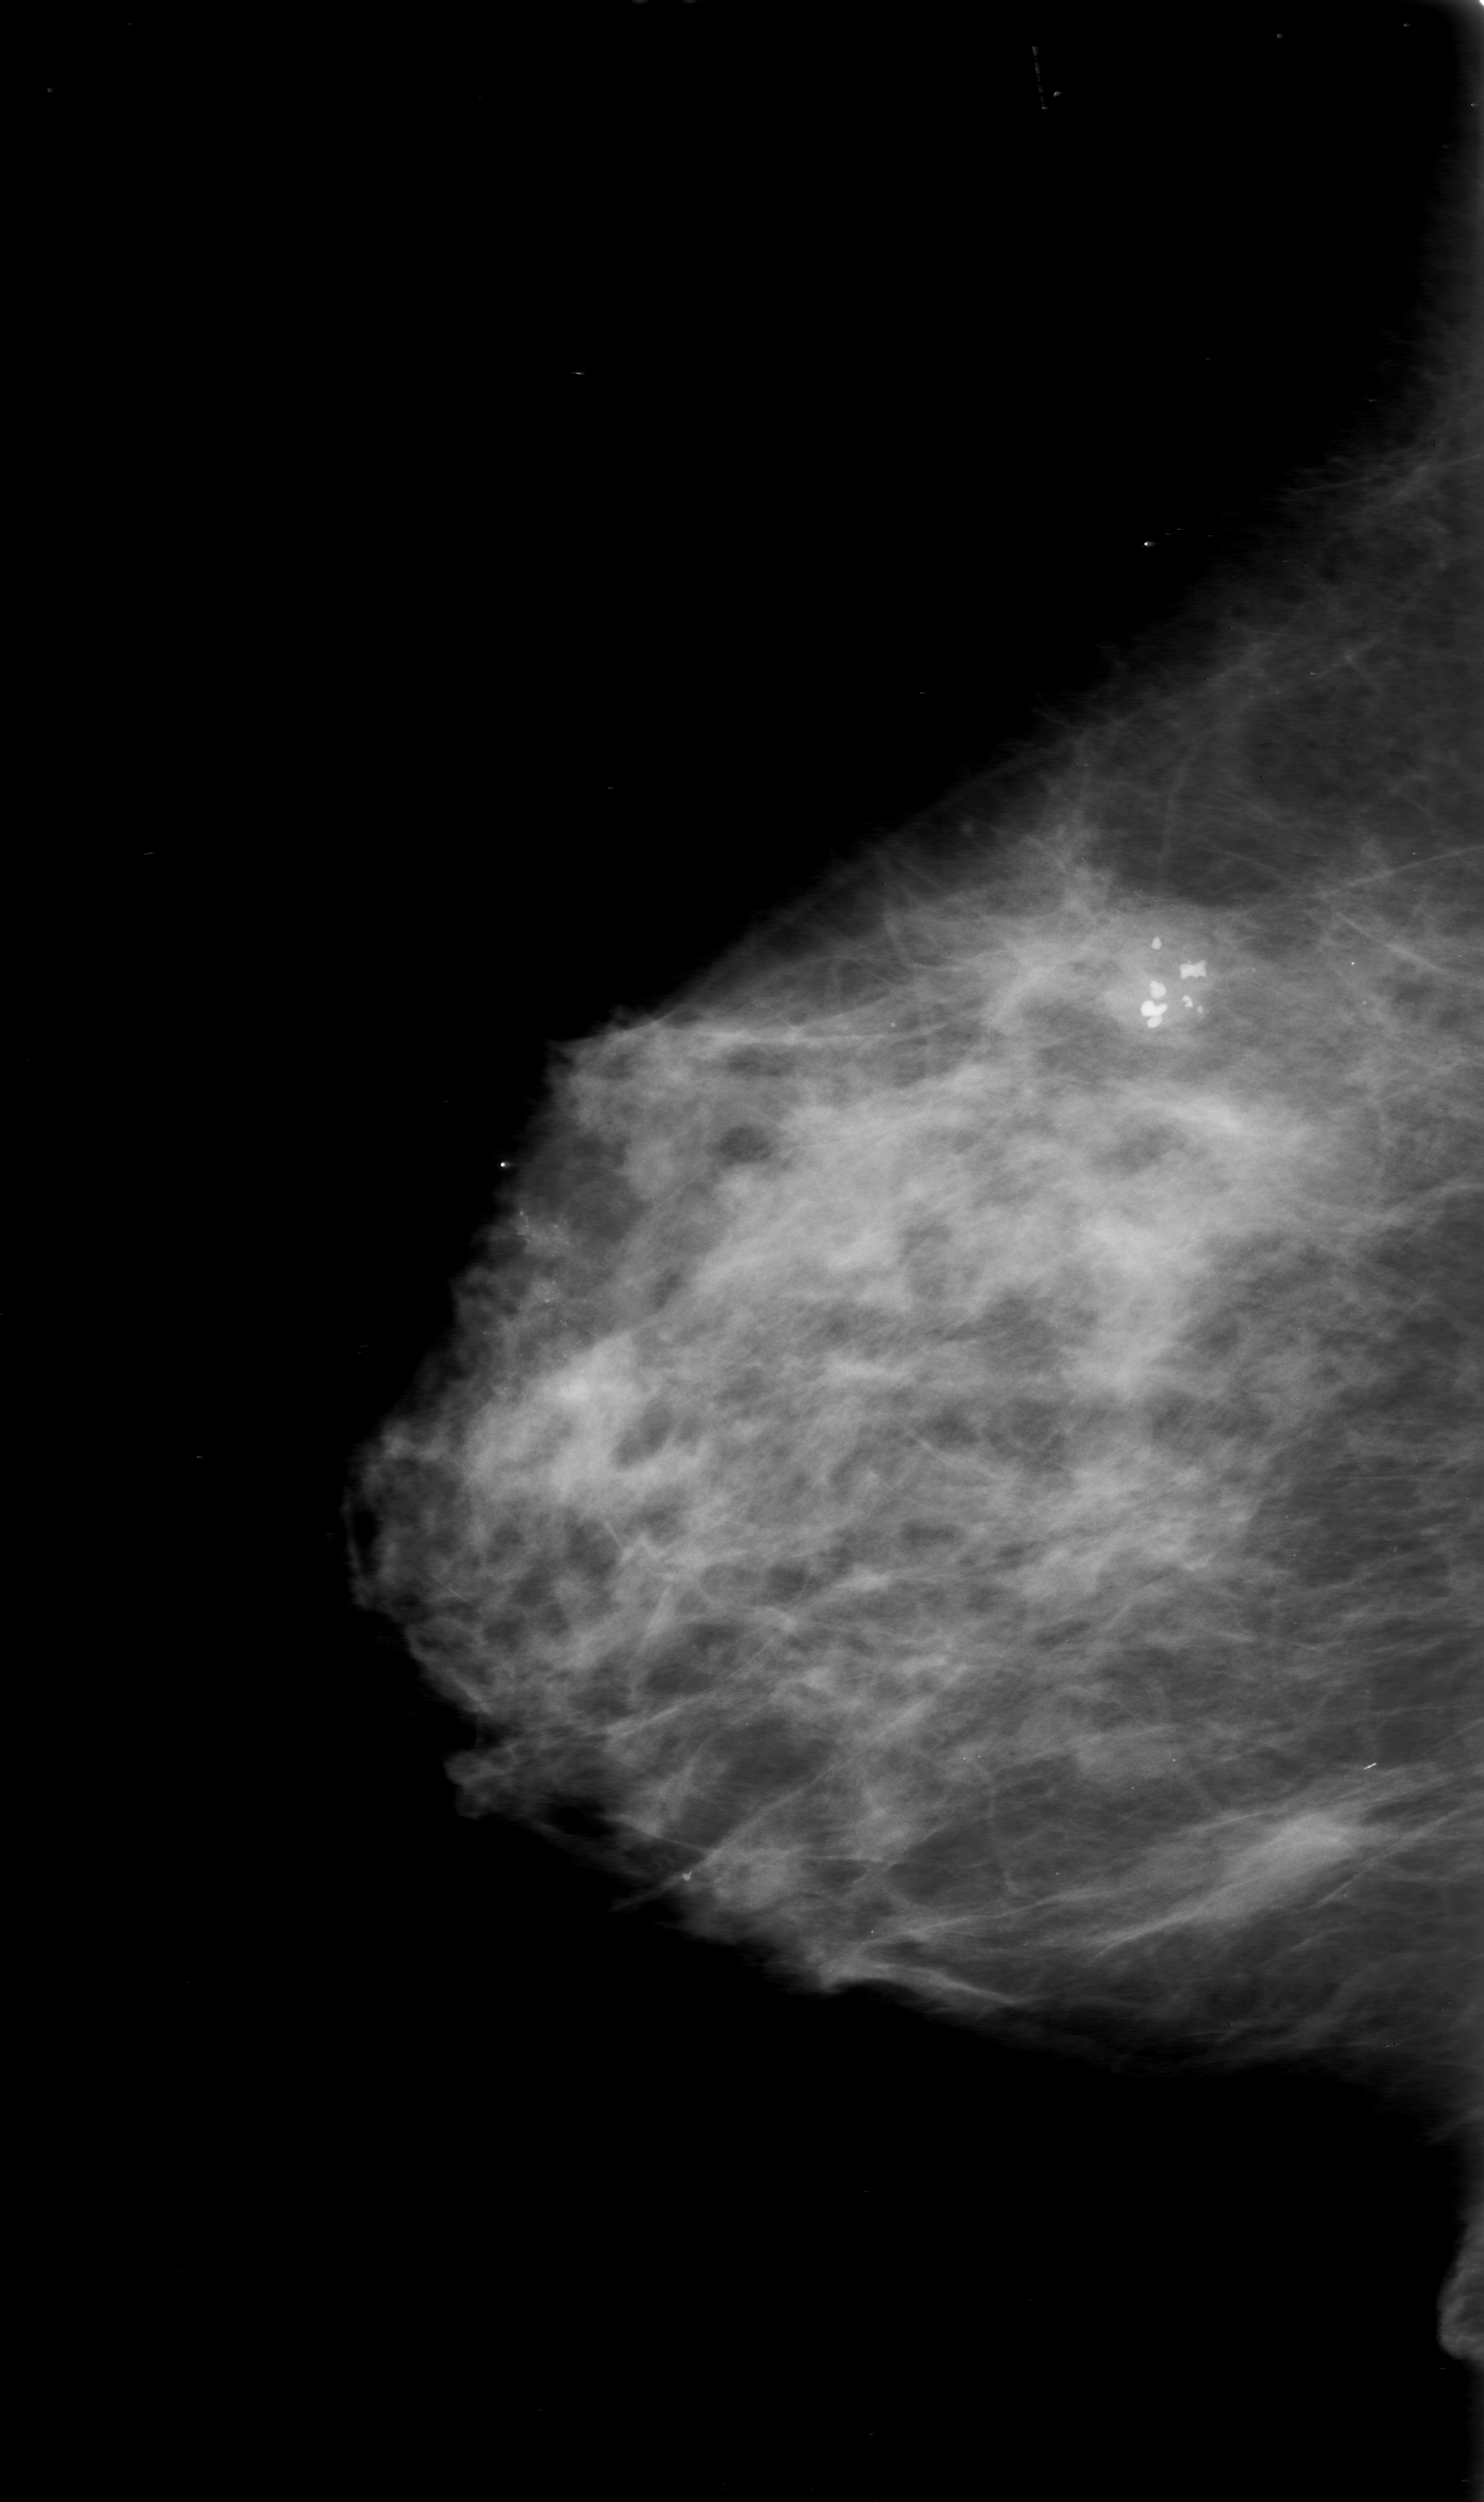
Mammogram (digitized film), right breast, MLO view, breast composition: heterogeneously dense (BI-RADS density category 3 of 4).
- Radiologist-marked abnormalities on this image: calcifications, morphology punctate / fine linear branching, distribution clustered; BI-RADS assessment category 0; subtlety rating 5 on a 1 (subtle) to 5 (obvious) scale; pathology (as recorded): malignant.